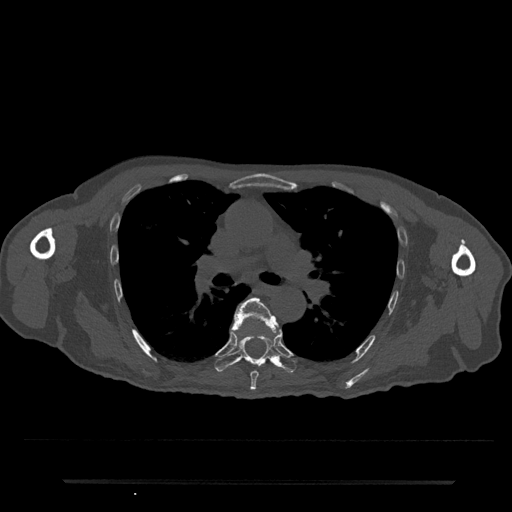
CT including the spine, one axial slice; slice 502 of 797 in the series (ordered by position); reconstruction kernel Br40s/3; 120 kVp; bone window (W 1800 / L 400 HU); 0.5 mm slice thickness; 512 × 512 image matrix, field of view 427 × 427 mm. Male patient, age 74 years. Case-level facts recorded for this patient, not image findings: primary cancer: prostate.
Outlined on this slice (semi-automatically segmented with operator editing):
- T6 vertebra: bounding box <231,297,279,391> (left, top, right, bottom; pixels)
- T7 vertebra: <215,329,297,373>